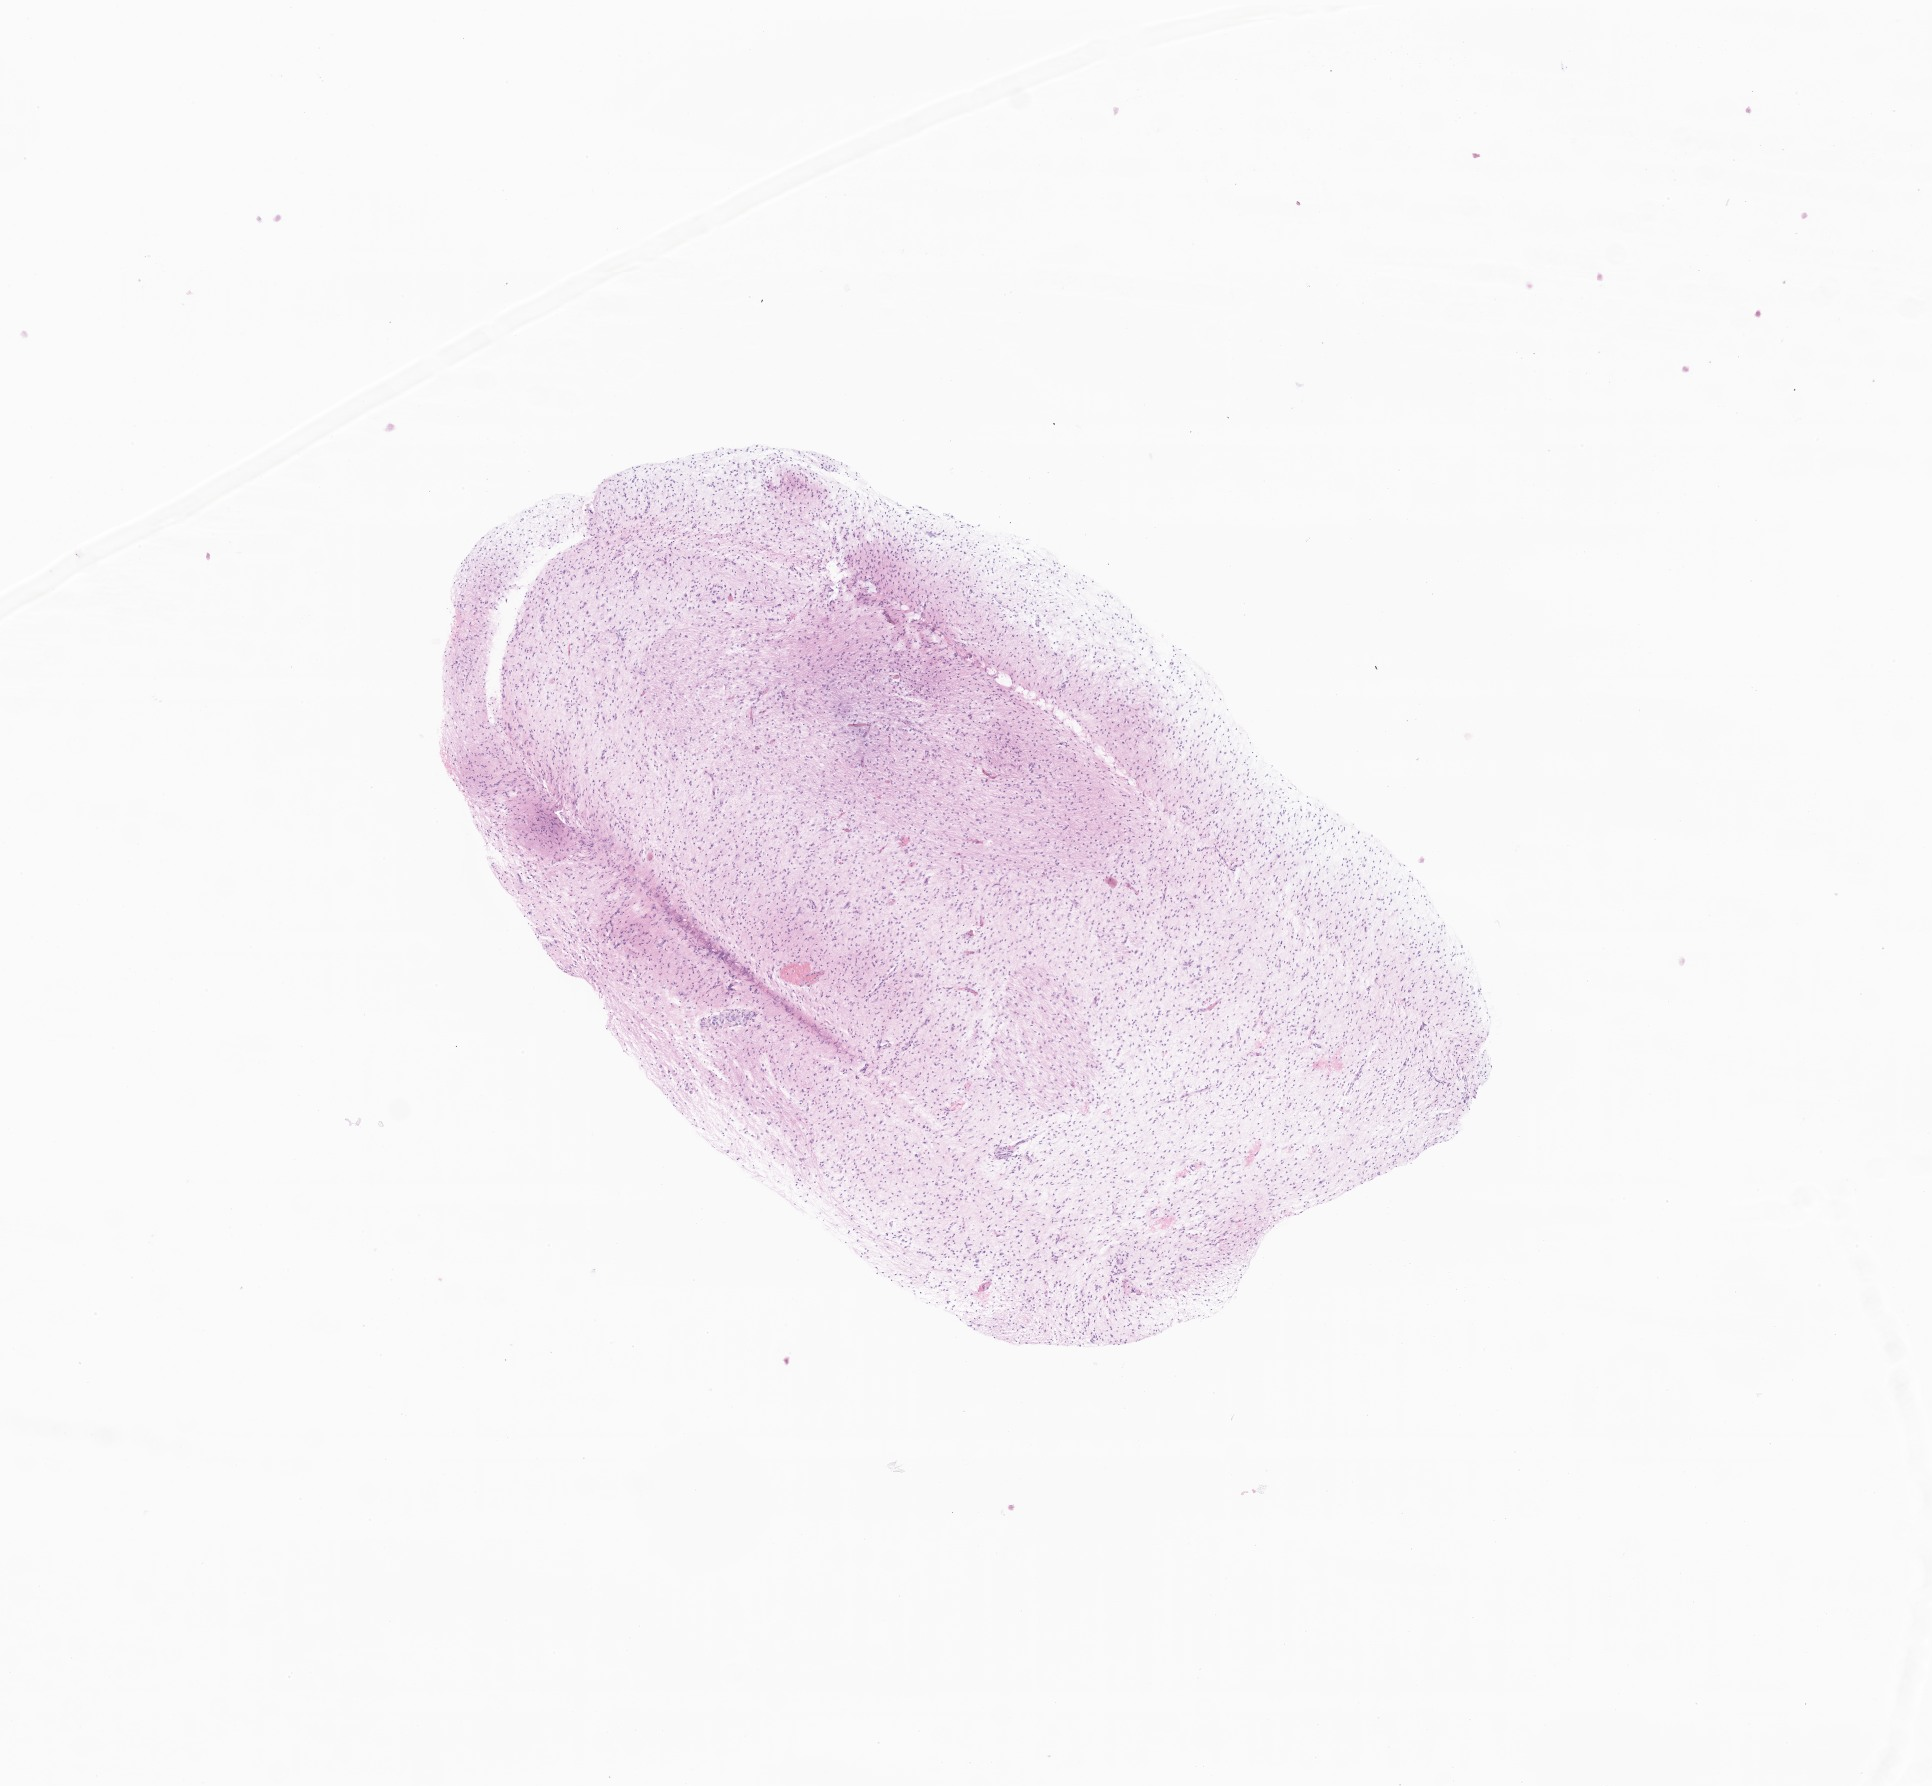
Digitized hematoxylin and eosin (H&E)-stained section of tumor tissue from the brain stem, whole scanned area (about 8.1 x 7.5 mm) shown as a low-resolution overview; formalin-fixed, paraffin-embedded (FFPE) tissue. Male patient, age 59 months (4 years 11 months).
• diagnosis: Glioma, malignant